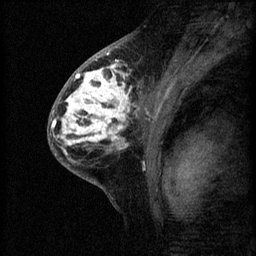
Breast MRI (dynamic contrast-enhanced), one sagittal slice; slice 34 of 60 in the series (ordered by position); 3 images stored at this slice position (order not interpretable as contrast timing); 1.5 T; TE 4.2 ms, TR 8.2 ms; 2 mm slice thickness; 256 × 256 image matrix, field of view 180 × 180 mm. Female patient, age 41 years.
Annotated regions visible in this slice (semi-automatic segmentation, software-assisted and operator-edited):
- analysis volume of interest (the breast-tissue region the enhancement analysis was run in; not a lesion): bounding box (x1, y1, x2, y2) in pixels: (53, 62, 160, 175)
- tumour enhancement mask (voxels above the 70 % enhancement threshold inside the analysis volume of interest): (53, 62, 148, 151)